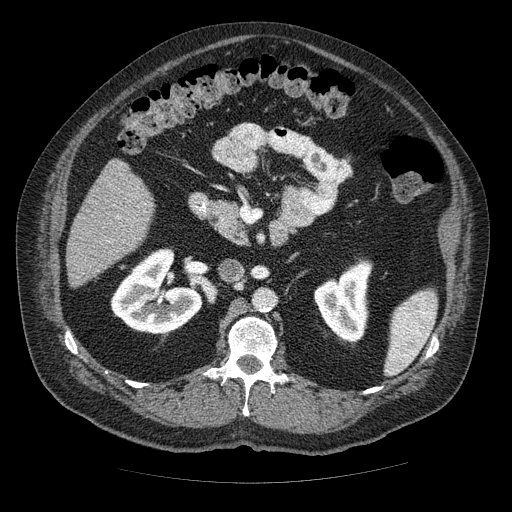
Contrast-enhanced abdominal CT (liver protocol), one axial slice. Position 18 of 85 along the scan axis. Reconstruction kernel STANDARD. 120 kVp. Soft-tissue window (W 400 / L 40 HU). 512 × 512 image matrix, field of view 420 × 420 mm. From the clinical record (not read from this slice): diagnosis: hepatocellular carcinoma (patient treated with transarterial chemoembolisation; whether this scan precedes or follows treatment is not stated here); TNM stage (as recorded): Stage-IIIA; Child-Pugh class: A; tumour nodularity: multinodular.
Outlined on this slice (semi-automatically segmented with operator editing):
- liver parenchyma outside the tumour (the mass and vessels are separate outlines, so this box may not span the whole liver): bounding box [x1, y1, x2, y2] px = [66, 160, 154, 286]
- liver vessels: [117, 216, 119, 218]